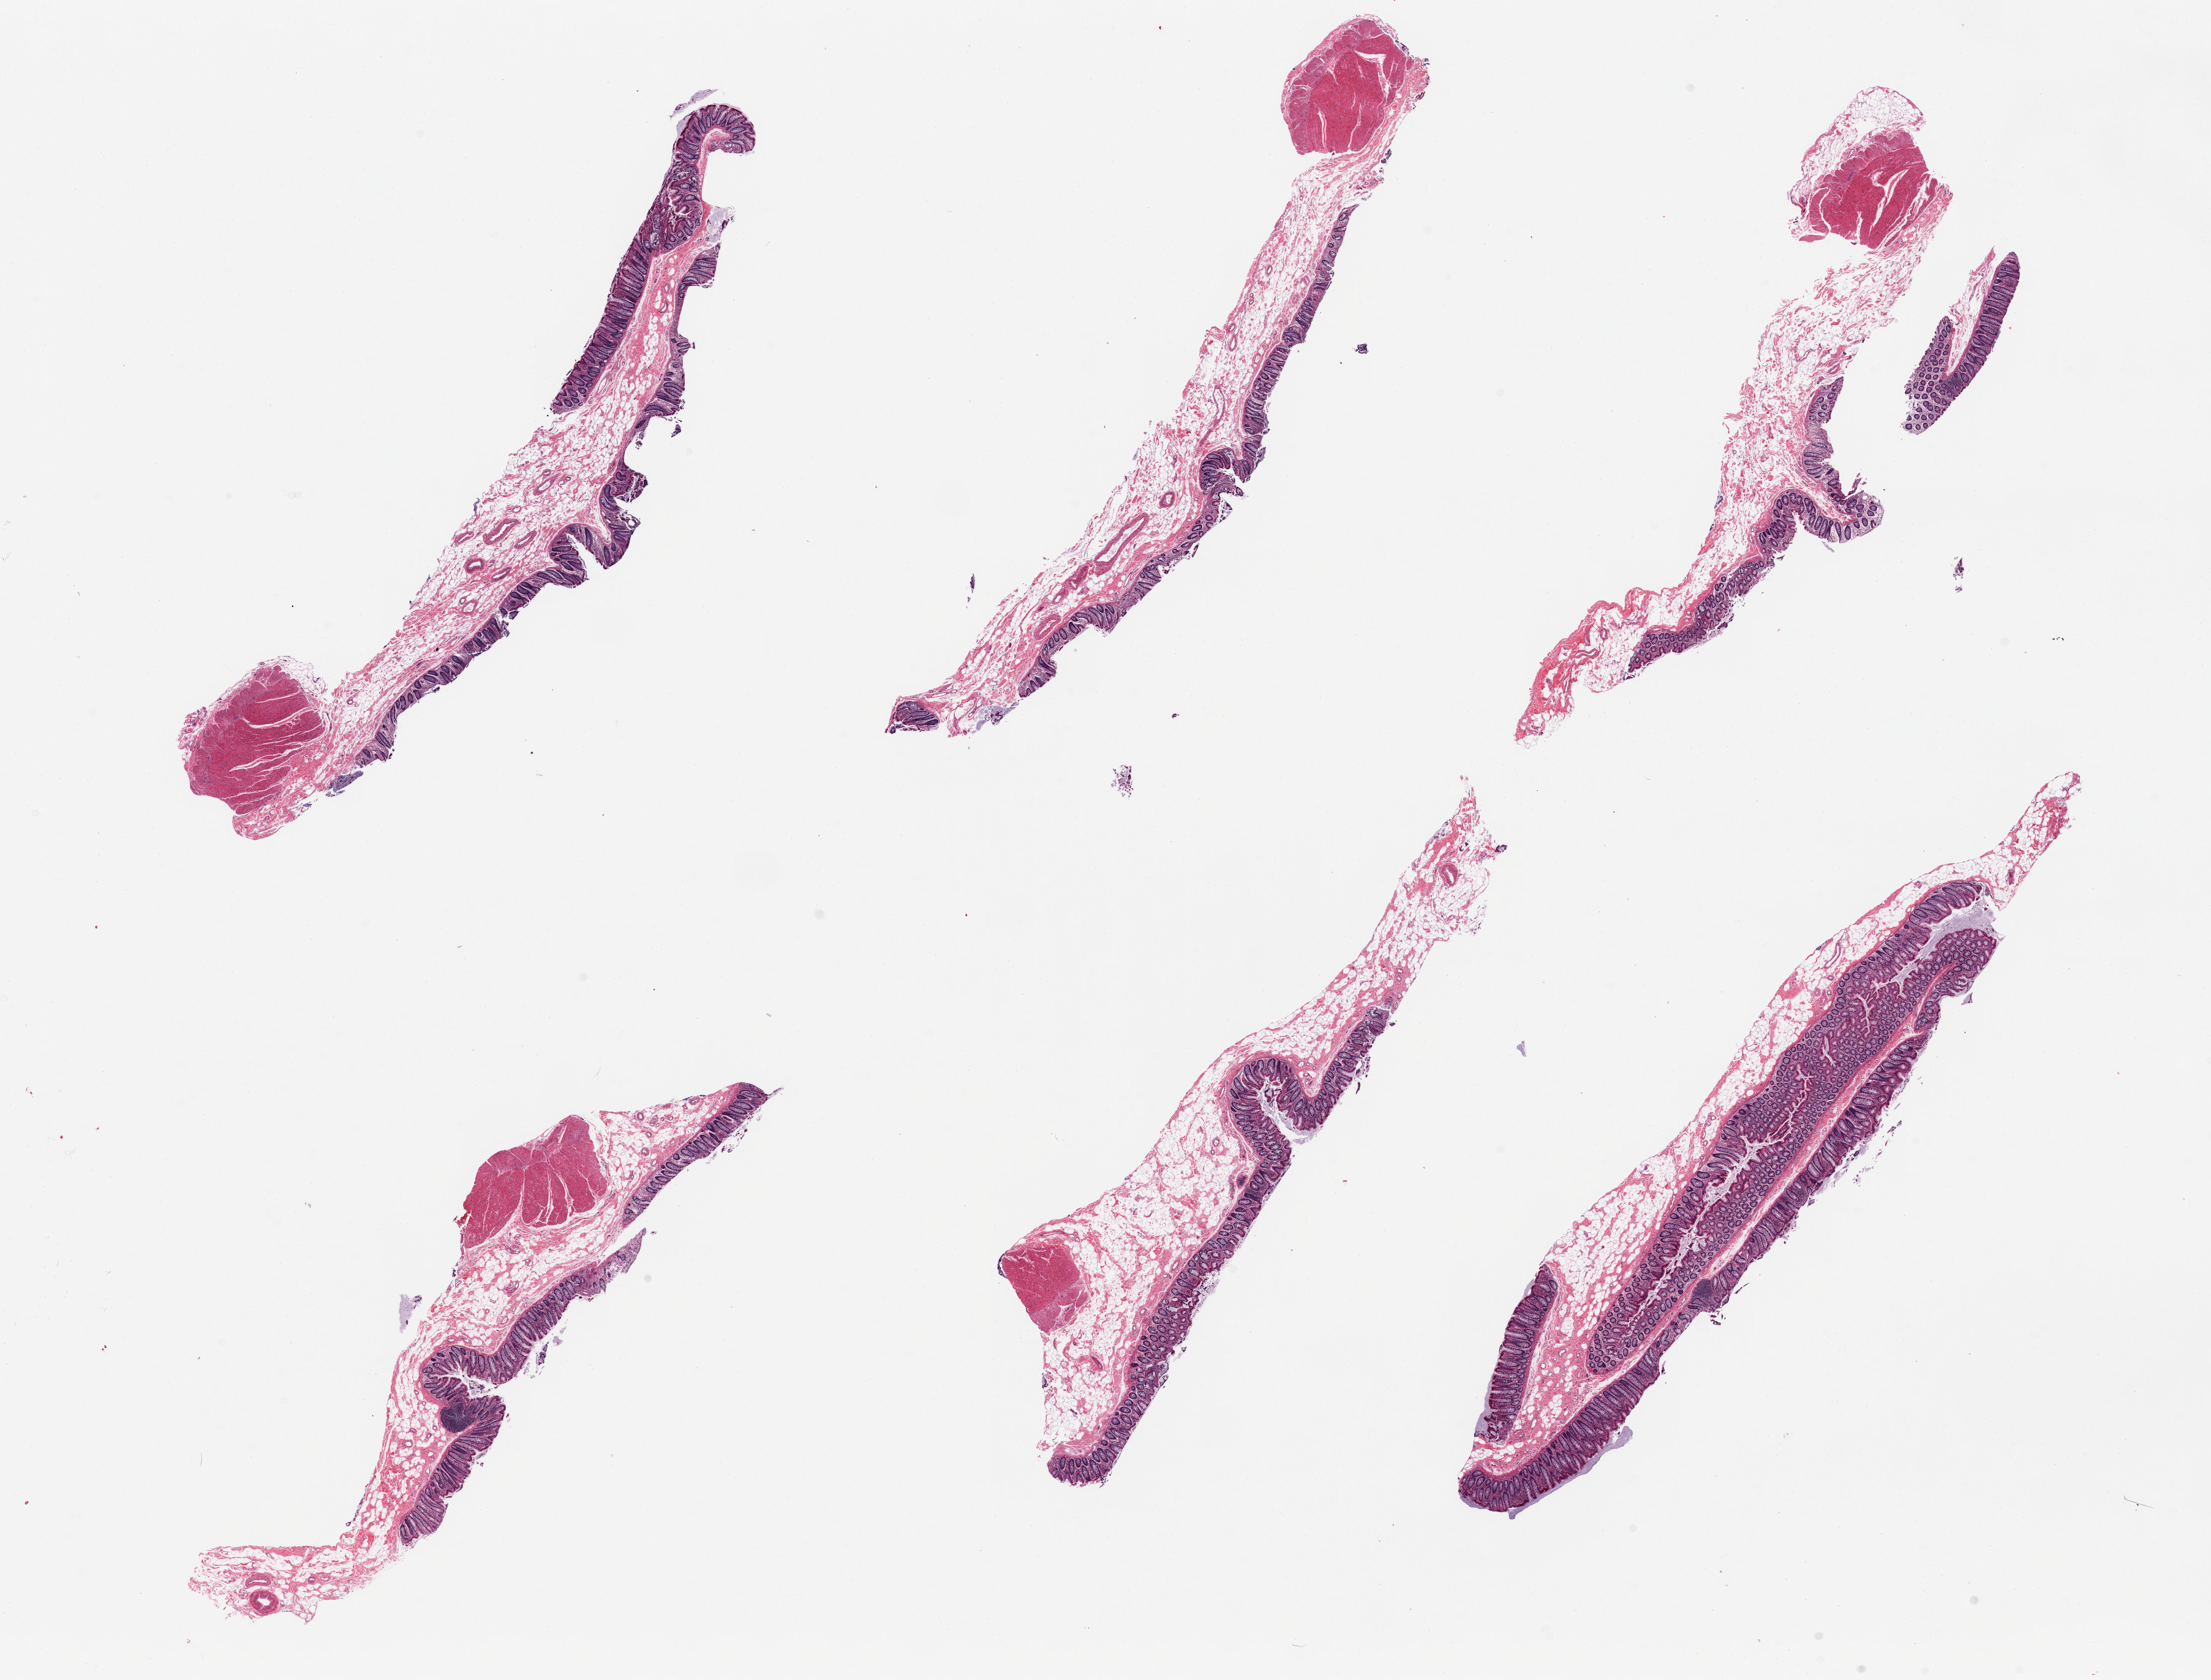
Whole-slide image, haematoxylin and eosin stain, brightfield, shown as a low-resolution overview of the whole scanned area (about 28.5 x 21.7 mm). PAXgene-fixed, paraffin-embedded tissue. Section of transverse colon (target tissue). Tissue donor sample.
Pathologist's review note for this sample: 6 pieces, mucosa well- preserved, up to ~0.5mm thick.